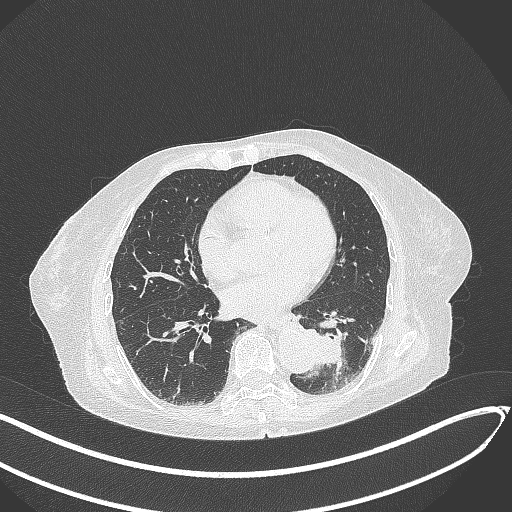
Chest CT, one axial slice; slice 101 of 324 in the series (ordered by position); reconstruction kernel B70f; lung window (W 1500 / L -600 HU); 1 mm slice thickness; 512 × 512 image matrix, field of view 400 × 400 mm. Female patient, age 82 years. Case-level facts recorded for this patient, not image findings: clinical TNM (as recorded): T1b N0 M1.
Structures marked on this image (bounding box drawn by a radiologist):
- lung tumour (recorded histology: adenocarcinoma): bounding box <298,324,354,374> (left, top, right, bottom; pixels)